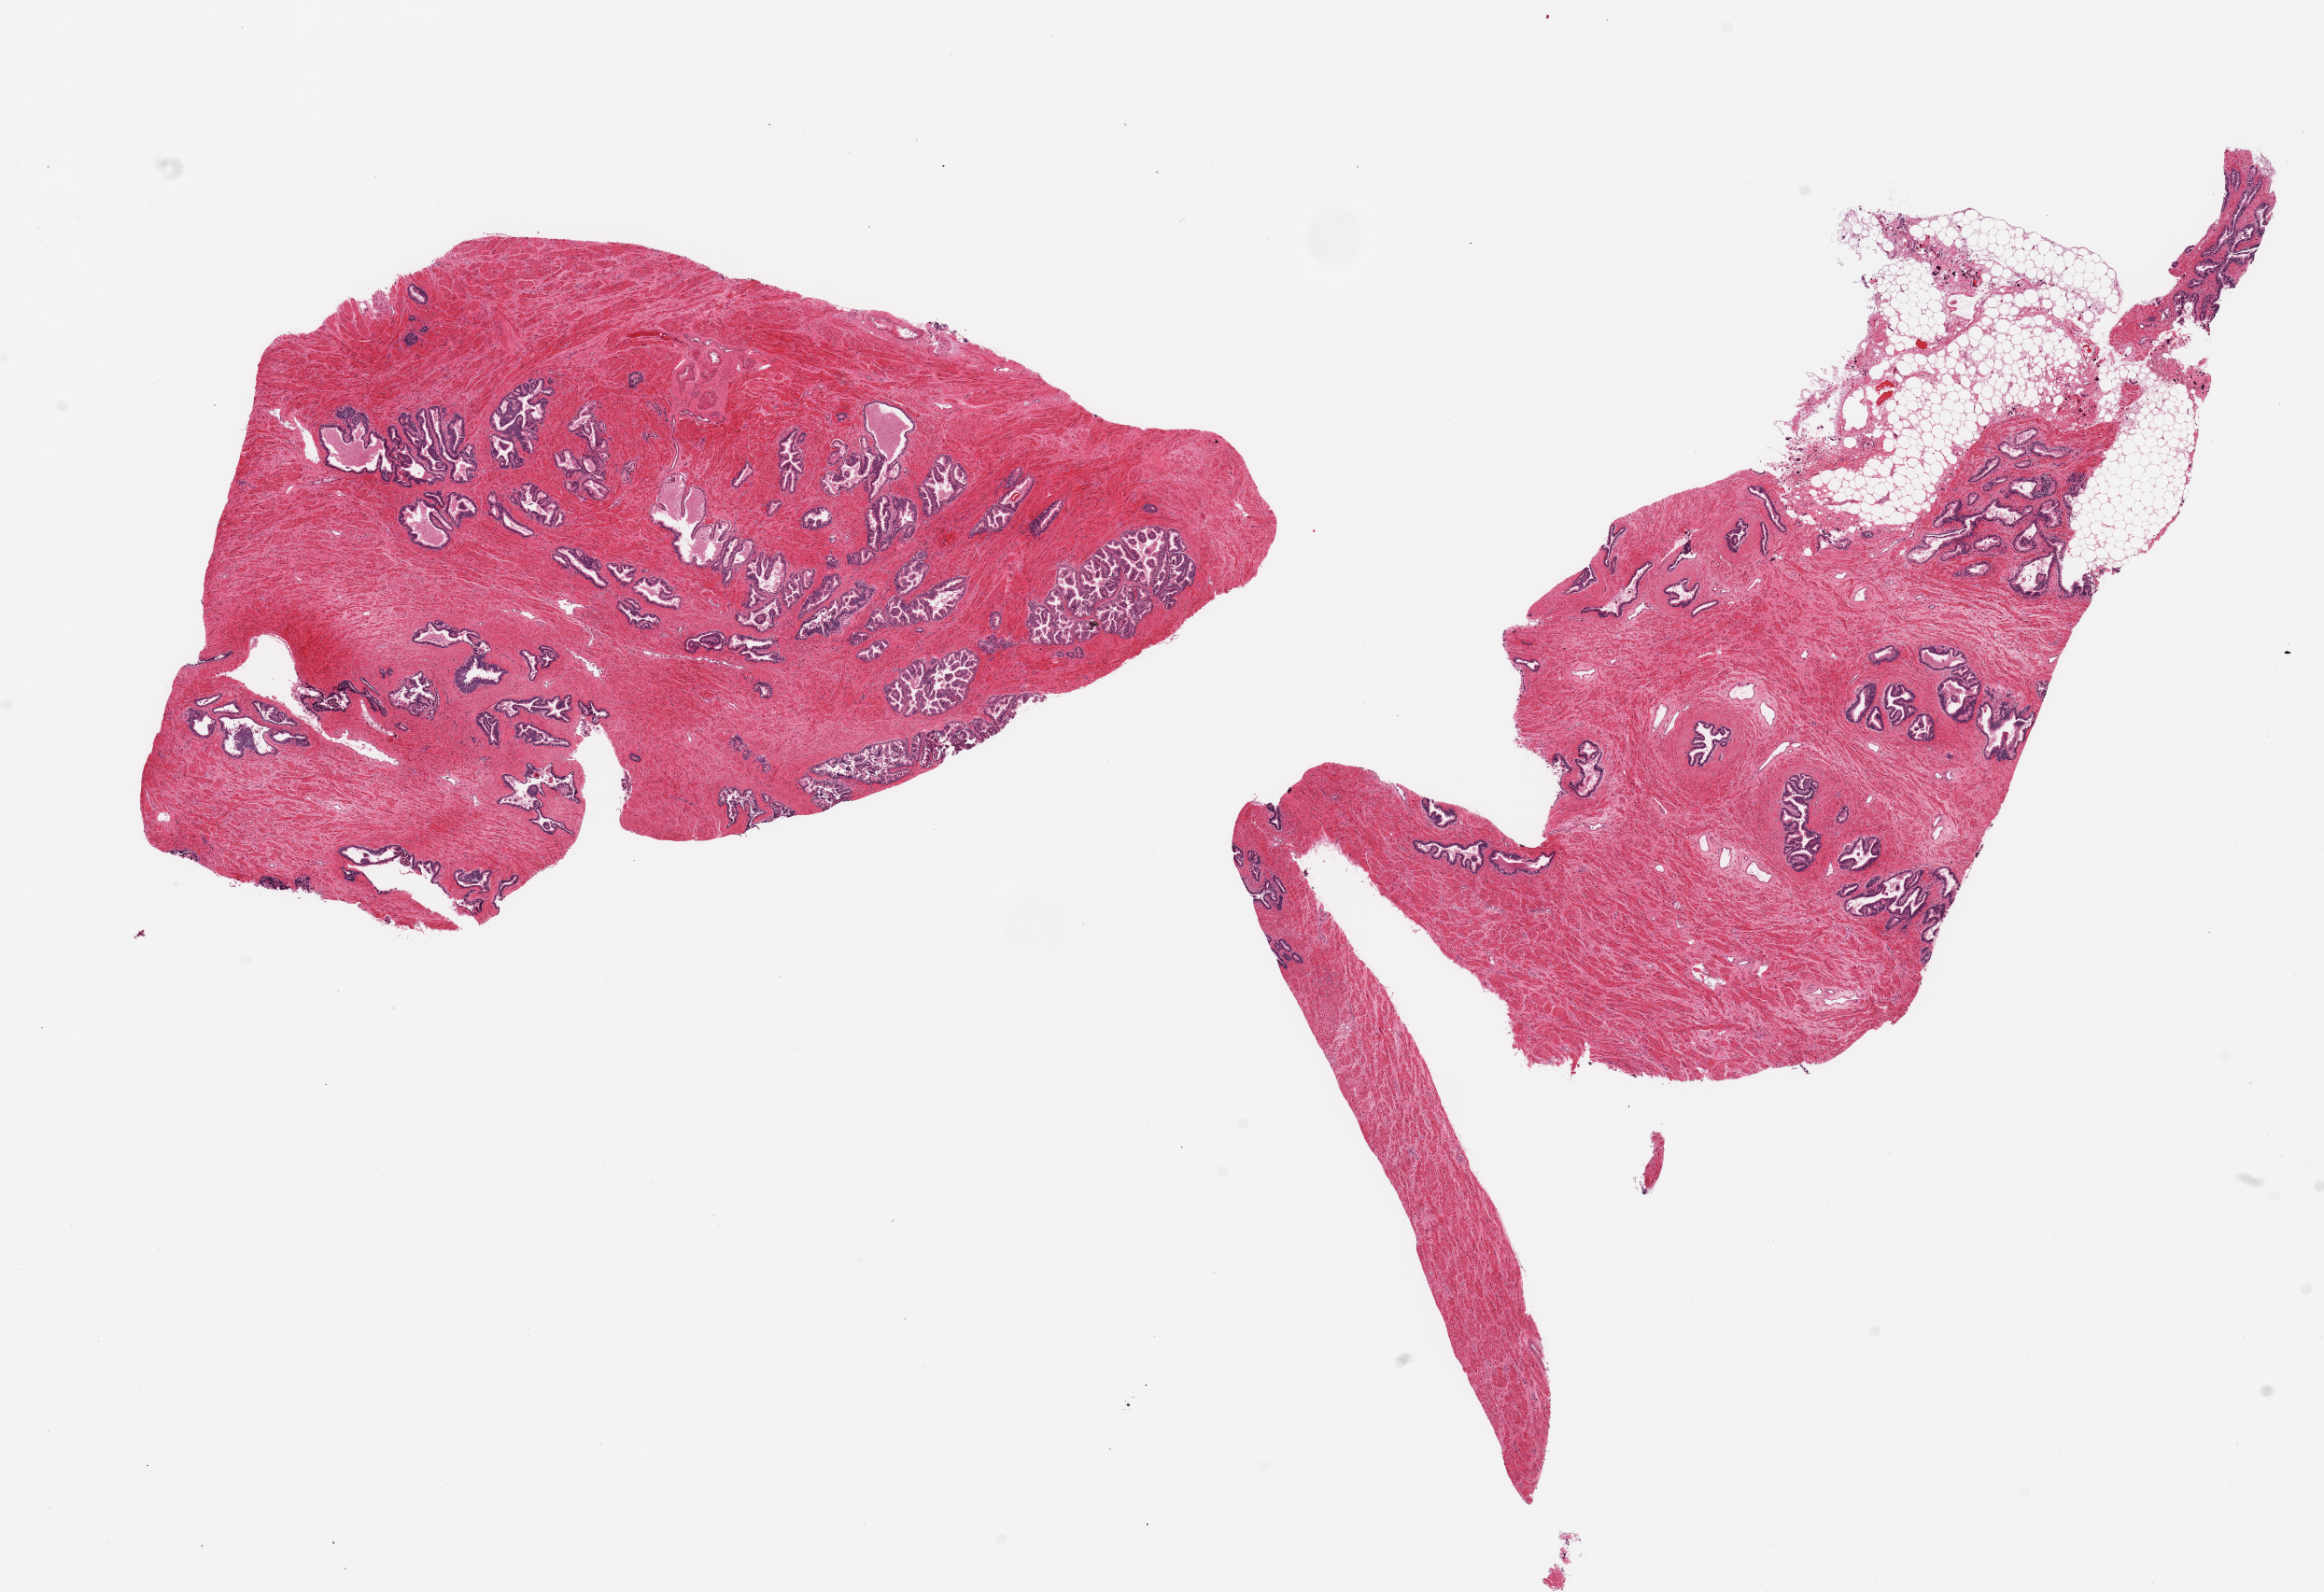
Digitized haematoxylin and eosin-stained section — whole scanned area (about 19.7 x 13.5 mm, acquisition: 20x scan) shown as a low-resolution overview, PAXgene-fixed, paraffin-embedded tissue, sampled site (target tissue): prostate, donor tissue sample.
Reviewer comment on this tissue sample: 2 pieces; hyperplastic glands; 20% external fat on 1 piece.